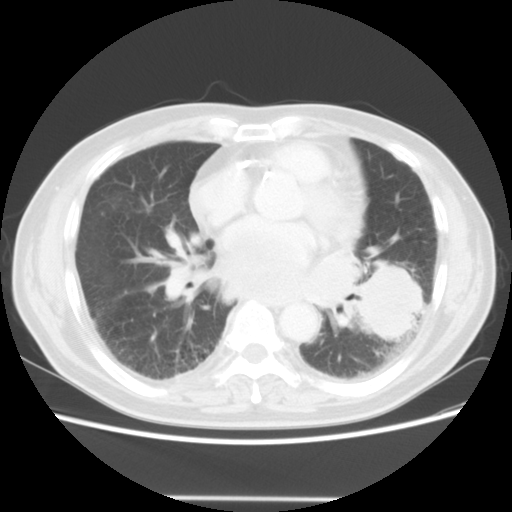
Chest CT, one axial slice; lung window (W 1500 / L -600 HU); 5 mm slice thickness; 512 × 512 image matrix, field of view 360 × 360 mm. Male patient, age 66 years. From the clinical record (not read from this slice): clinical TNM (as recorded): T4 N3 M0.
Annotated regions visible in this slice (bounding box drawn by a radiologist):
- lung tumour (recorded histology: small cell carcinoma): bounding box [x1, y1, x2, y2] px = [349, 265, 434, 345]